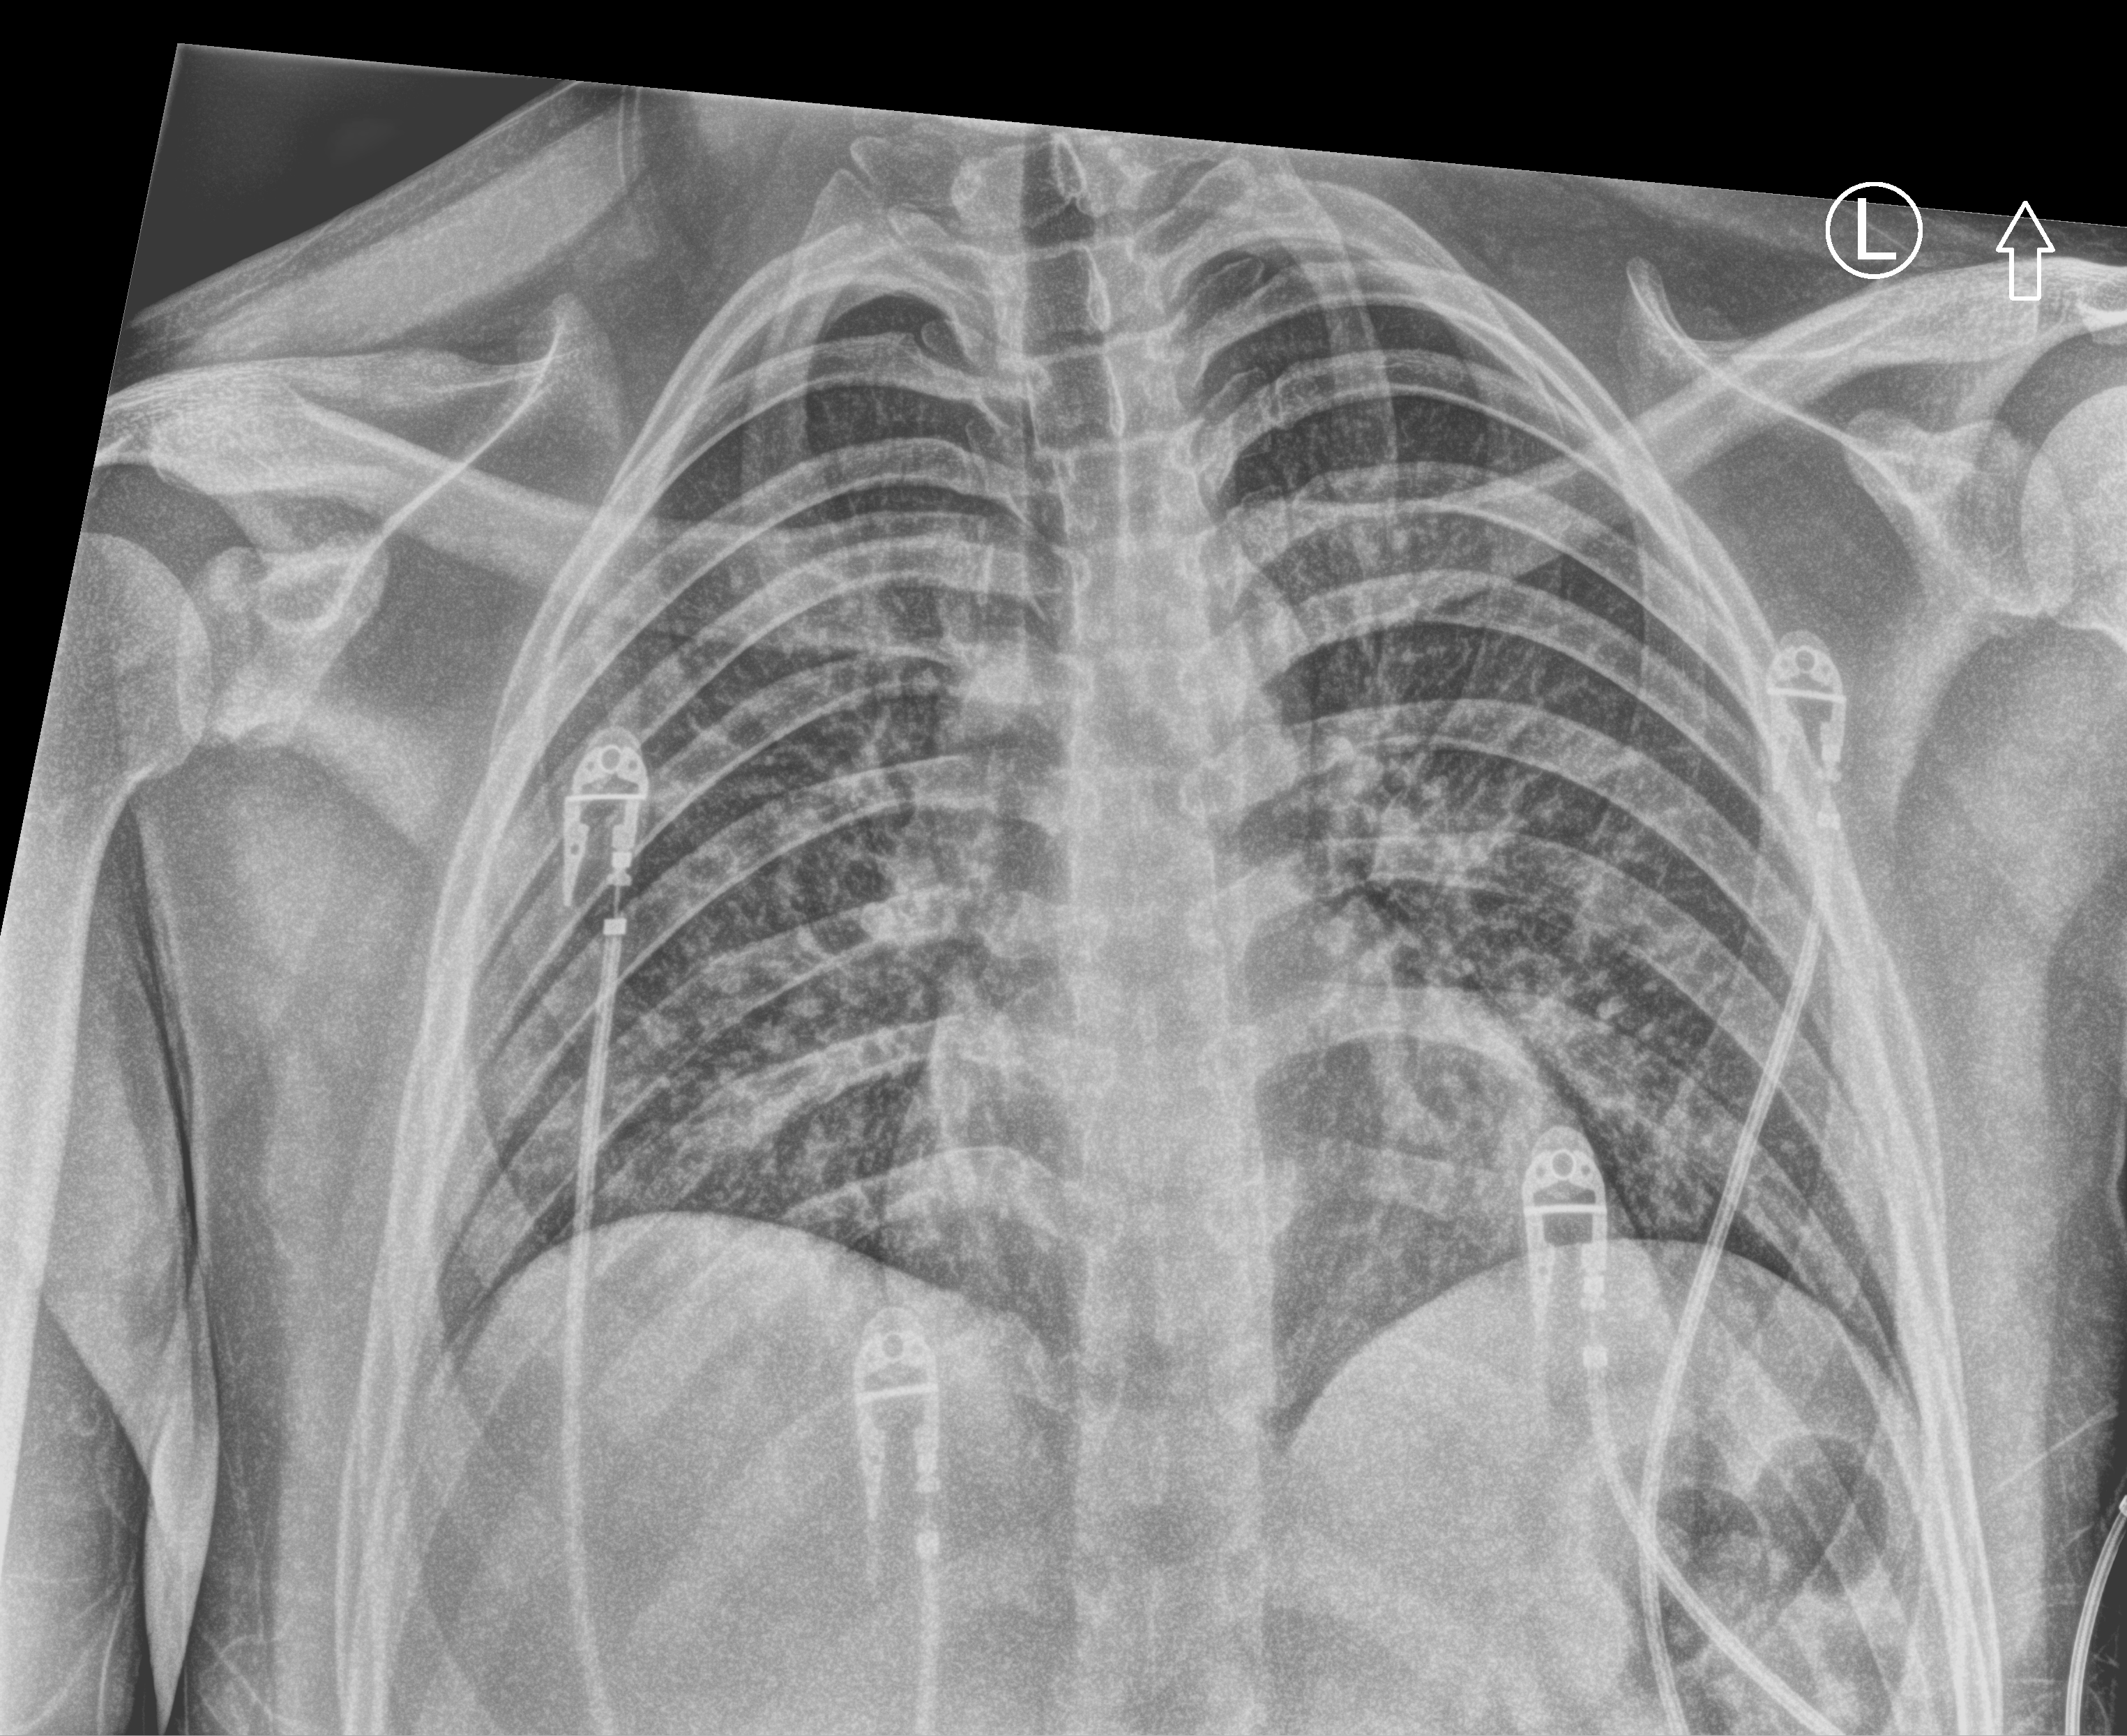
Portable chest radiograph, anteroposterior (AP) projection. Patient hospitalised with COVID-19; male, aged 18–59 years.
Admission-level facts for this patient (not findings on this image; timing relative to this image not recorded):
- mechanically ventilated during this hospital stay: no